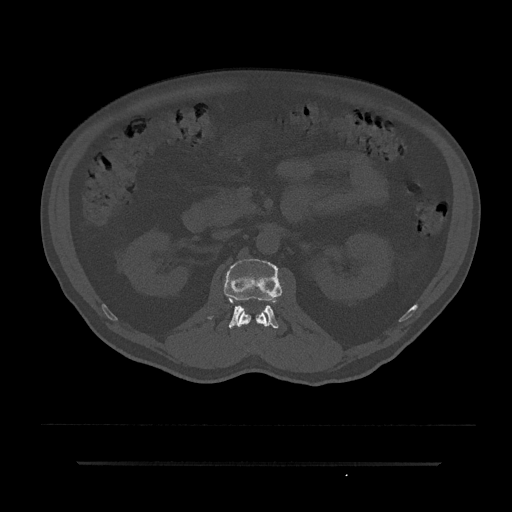
CT including the spine, one axial slice. Bone window (W 1800 / L 400 HU). 512 × 512 image matrix. Male patient, age 59 years. Case-level facts recorded for this patient, not image findings: primary cancer: bile ducts.
Annotated regions visible in this slice (semi-automatically segmented with operator editing):
- L1 vertebra: bounding box (x1, y1, x2, y2) in pixels: (238, 310, 268, 346)
- L2 vertebra: (210, 258, 282, 329)